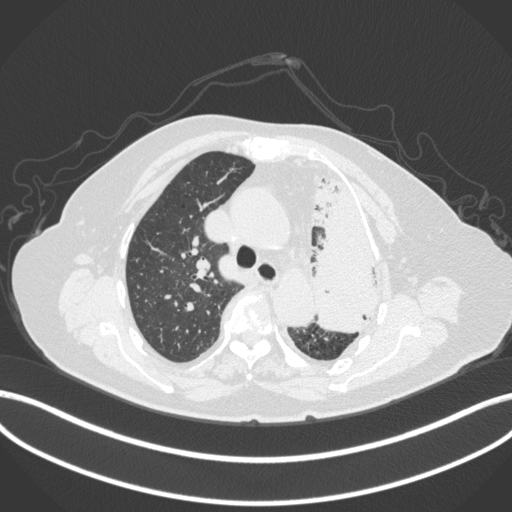
Chest CT, one axial slice; position 281 of 399 along the scan axis; reconstruction kernel B31f; 120 kVp; lung window (W 1500 / L -600 HU); 1 mm slice thickness; 512 × 512 image matrix, field of view 400 × 400 mm. Patient: female, 75 years. From the clinical record (not read from this slice): clinical TNM (as recorded): T3 N3 M1.
Structures marked on this image (rectangle marked by the reading radiologist):
- lung tumour (recorded histology: adenocarcinoma): box from (x=305, y=165) to (x=394, y=339) px